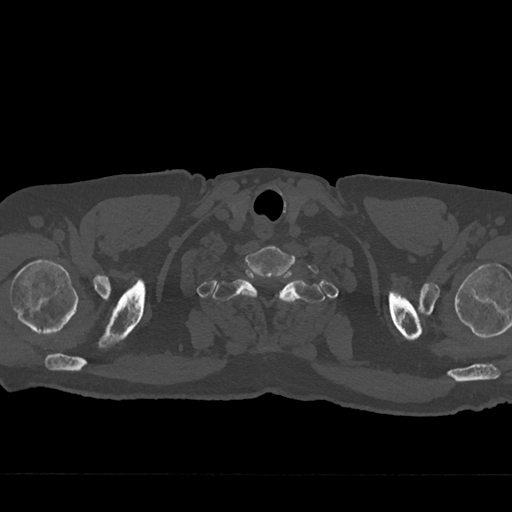
CT including the spine, one axial slice; reconstruction kernel Br40s/3; bone window (W 1800 / L 400 HU); 0.5 mm slice thickness; 512 × 512 image matrix. Patient: male, 75 years. Case-level facts recorded for this patient, not image findings: primary cancer: renal; vertebrae with lytic lesions (as recorded): T4.
Outlined on this slice (semi-automatically segmented with operator editing):
- T1 vertebra: bounding box (x1, y1, x2, y2) in pixels: (213, 271, 325, 303)